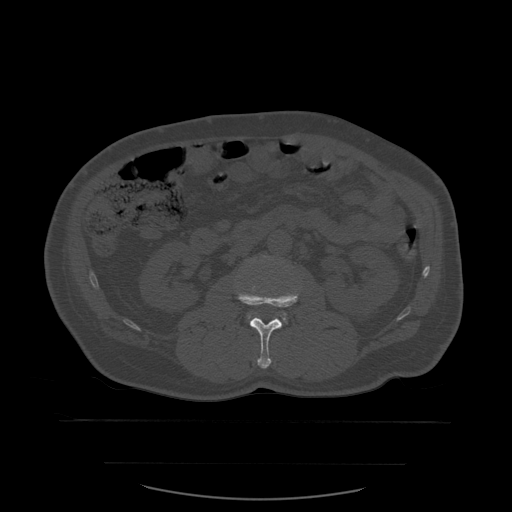
CT including the spine, one axial slice. Position 211 of 590 along the scan axis. Bone window (W 1800 / L 400 HU). 512 × 512 image matrix. Patient age 71 years. From the clinical record (not read from this slice): primary cancer: lung.
Annotated regions visible in this slice (semi-automatically segmented with operator editing):
- L2 vertebra: box from (x=238, y=274) to (x=299, y=369) px
- L3 vertebra: (x=248, y=256)–(x=287, y=321)